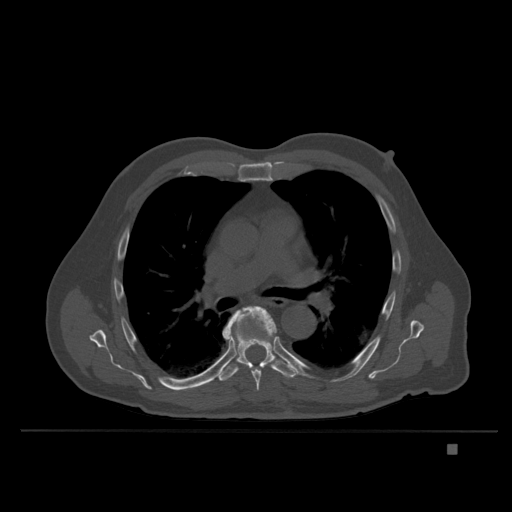
CT including the spine, one axial slice. Slice 251 of 435 in the series (ordered by position). Bone window (W 1800 / L 400 HU). 1.5 mm slice thickness. 512 × 512 image matrix, field of view 434 × 434 mm. Patient: male, 73 years. From the clinical record (not read from this slice): primary cancer: skin.
Structures marked on this image (semi-automatic segmentation, software-assisted and operator-edited):
- T6 vertebra: bounding box [x1, y1, x2, y2] px = [222, 306, 277, 391]
- T7 vertebra: [210, 306, 300, 382]